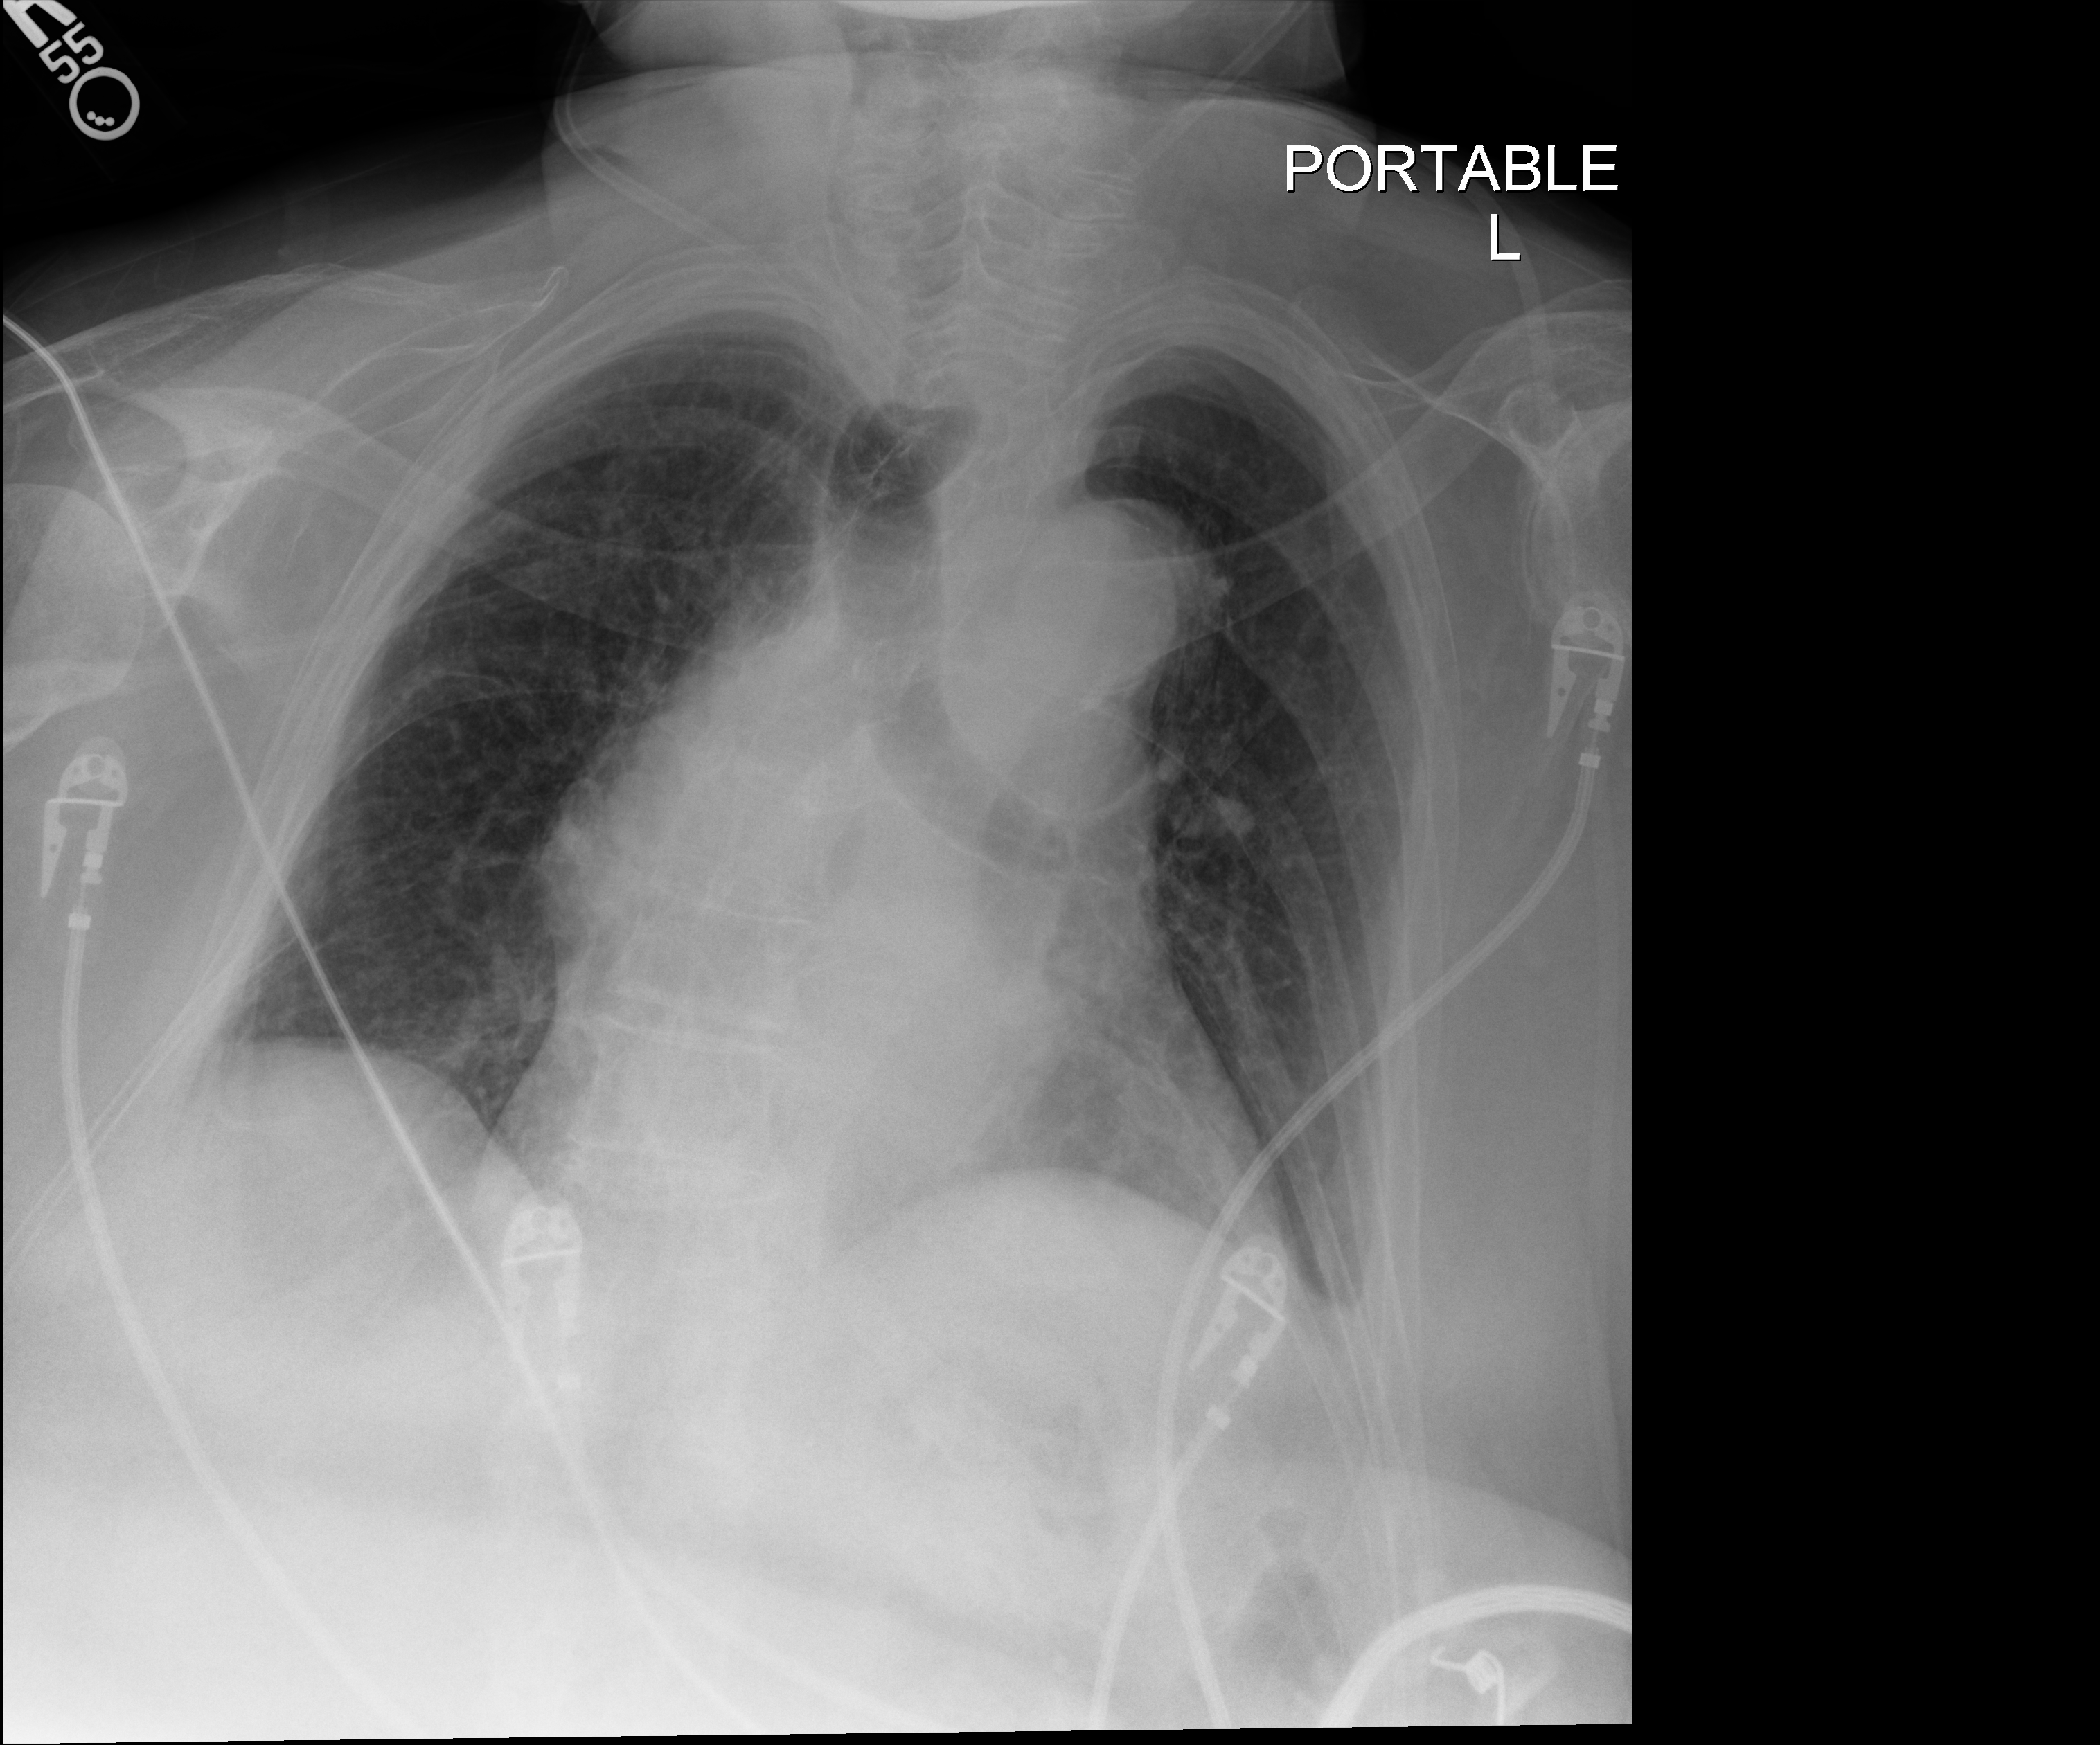
Chest X-ray (portable); anteroposterior (AP) projection. Patient hospitalised with COVID-19; female, aged 75–90 years.
Hospital-stay facts (about this admission, not read from this image; timing relative to this image not recorded): mechanically ventilated during this hospital stay: no.